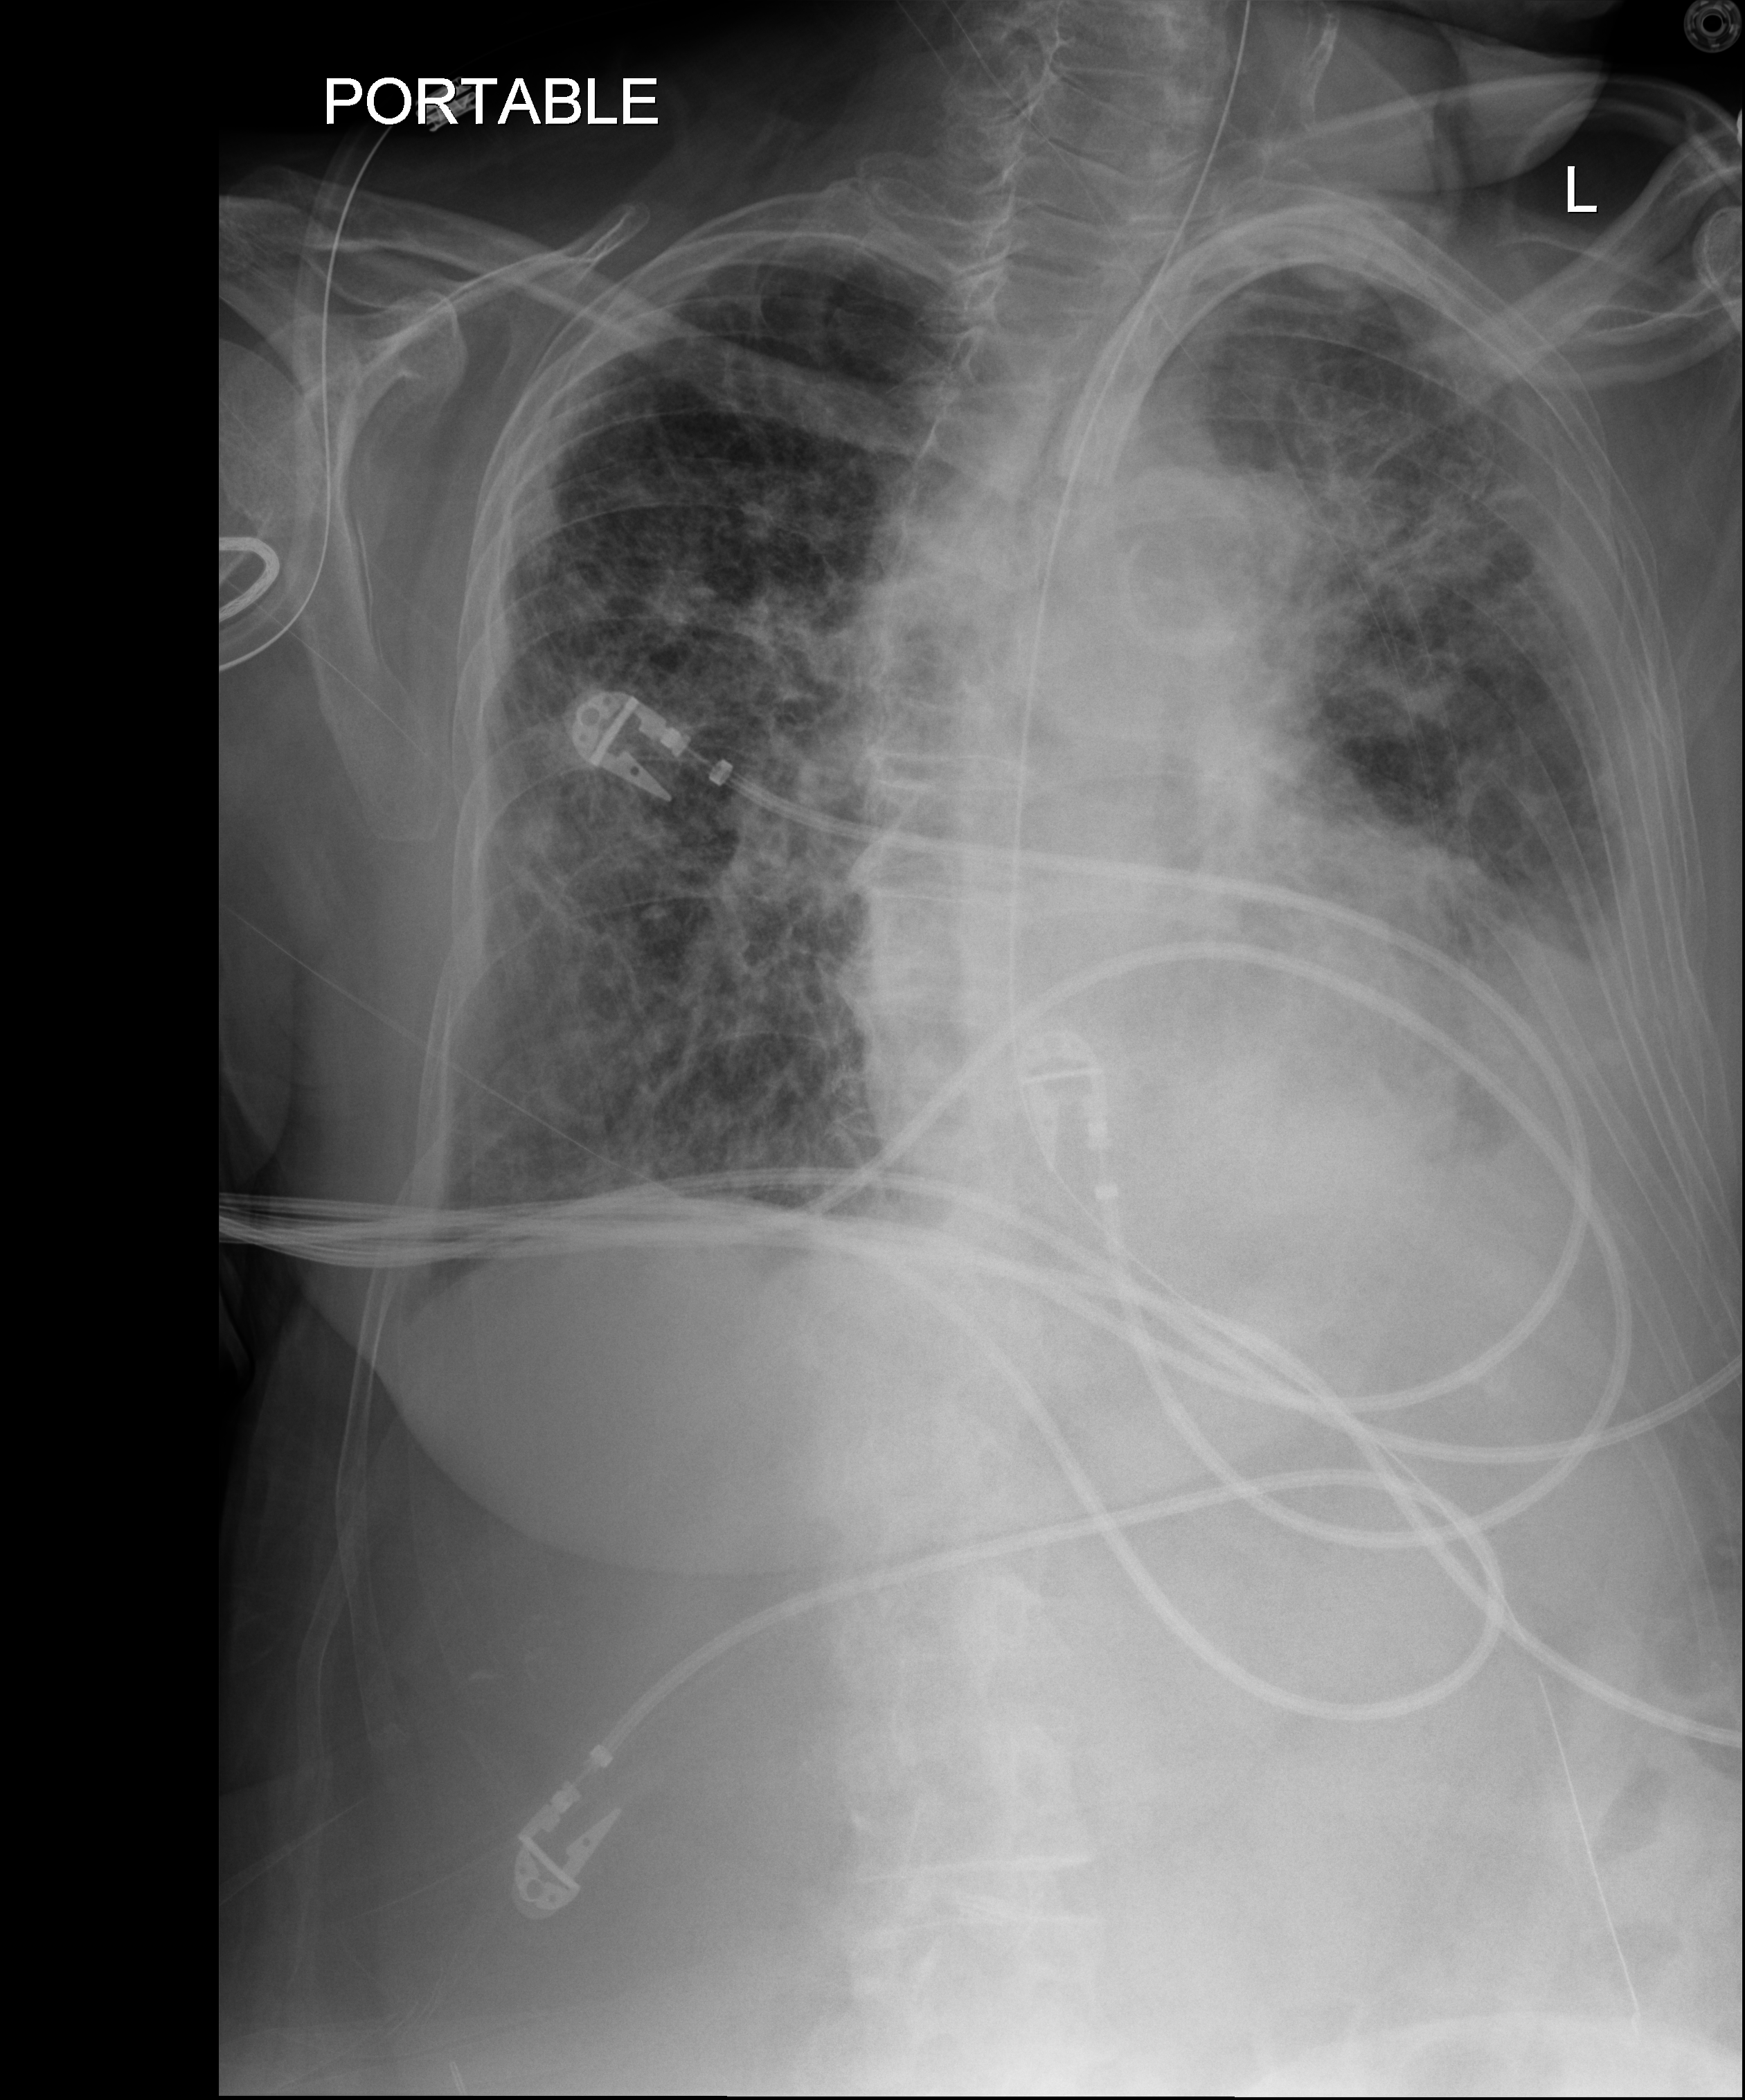
Portable chest radiograph; anteroposterior (AP) projection. Patient hospitalised with COVID-19; female, aged 75–90 years.
Admission-level facts for this patient (not findings on this image; timing relative to this image not recorded):
- admitted to intensive care during this hospital stay: yes